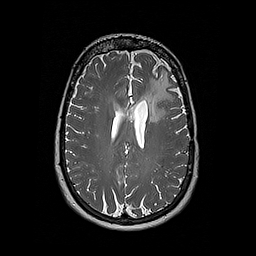
Brain MRI from a brain-tumour surgery series, one axial slice; 1 mm slice thickness; 256 × 256 image matrix. Case-level facts recorded for this patient, not image findings: histopathology: Oligodendroglioma; WHO grade: 2; IDH mutation: yes.
Outlined on this slice (expert manual segmentation):
- tumour: bounding box <143,77,165,122> (left, top, right, bottom; pixels)